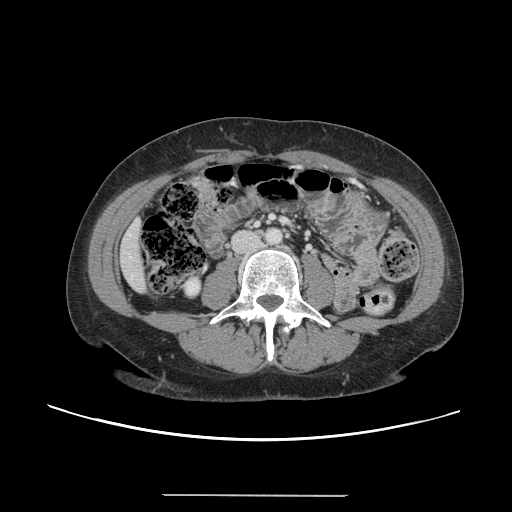
Contrast-enhanced abdominal CT, one axial slice; slice 20 of 144 in the series (ordered by position); intravenous contrast given; soft-tissue window (W 400 / L 40 HU); 2.5 mm slice thickness; 512 × 512 image matrix. Female patient, age 53 years. Case-level facts recorded for this patient, not image findings: diagnosis: colorectal cancer liver metastases, imaged before liver resection; multiple liver metastases: yes; largest metastasis: 1.1 cm; disease in both lobes: no.
Structures marked on this image (outlined manually by an expert reader):
- liver: bounding box <120,220,146,293> (left, top, right, bottom; pixels)
- planned liver remnant (the part of the liver to remain after resection): <120,220,146,294>